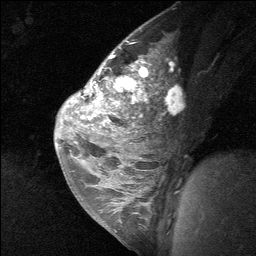
Breast MRI (dynamic contrast-enhanced), one sagittal slice; position 42 of 64 along the scan axis; dynamic contrast-enhanced study with each time point stored as its own series, time point 2 of 3 at this slice position (early post-contrast, ordered by acquisition time); 1.5 T; TE 4.8 ms, TR 27 ms; 2 mm slice thickness; 256 × 256 image matrix, field of view 180 × 180 mm. Female patient, age 26 years. From the clinical record (not read from this slice): setting: breast cancer imaged before/during neoadjuvant chemotherapy; receptor status: HR-positive, HER2-negative.
Outlined on this slice (semi-automatically segmented with operator editing):
- analysis volume of interest (the breast-tissue region the enhancement analysis was run in; not a lesion): bounding box [x1, y1, x2, y2] px = [86, 43, 164, 138]
- tumour enhancement mask (voxels above the 90 % enhancement threshold inside the analysis volume of interest): [89, 56, 148, 120]